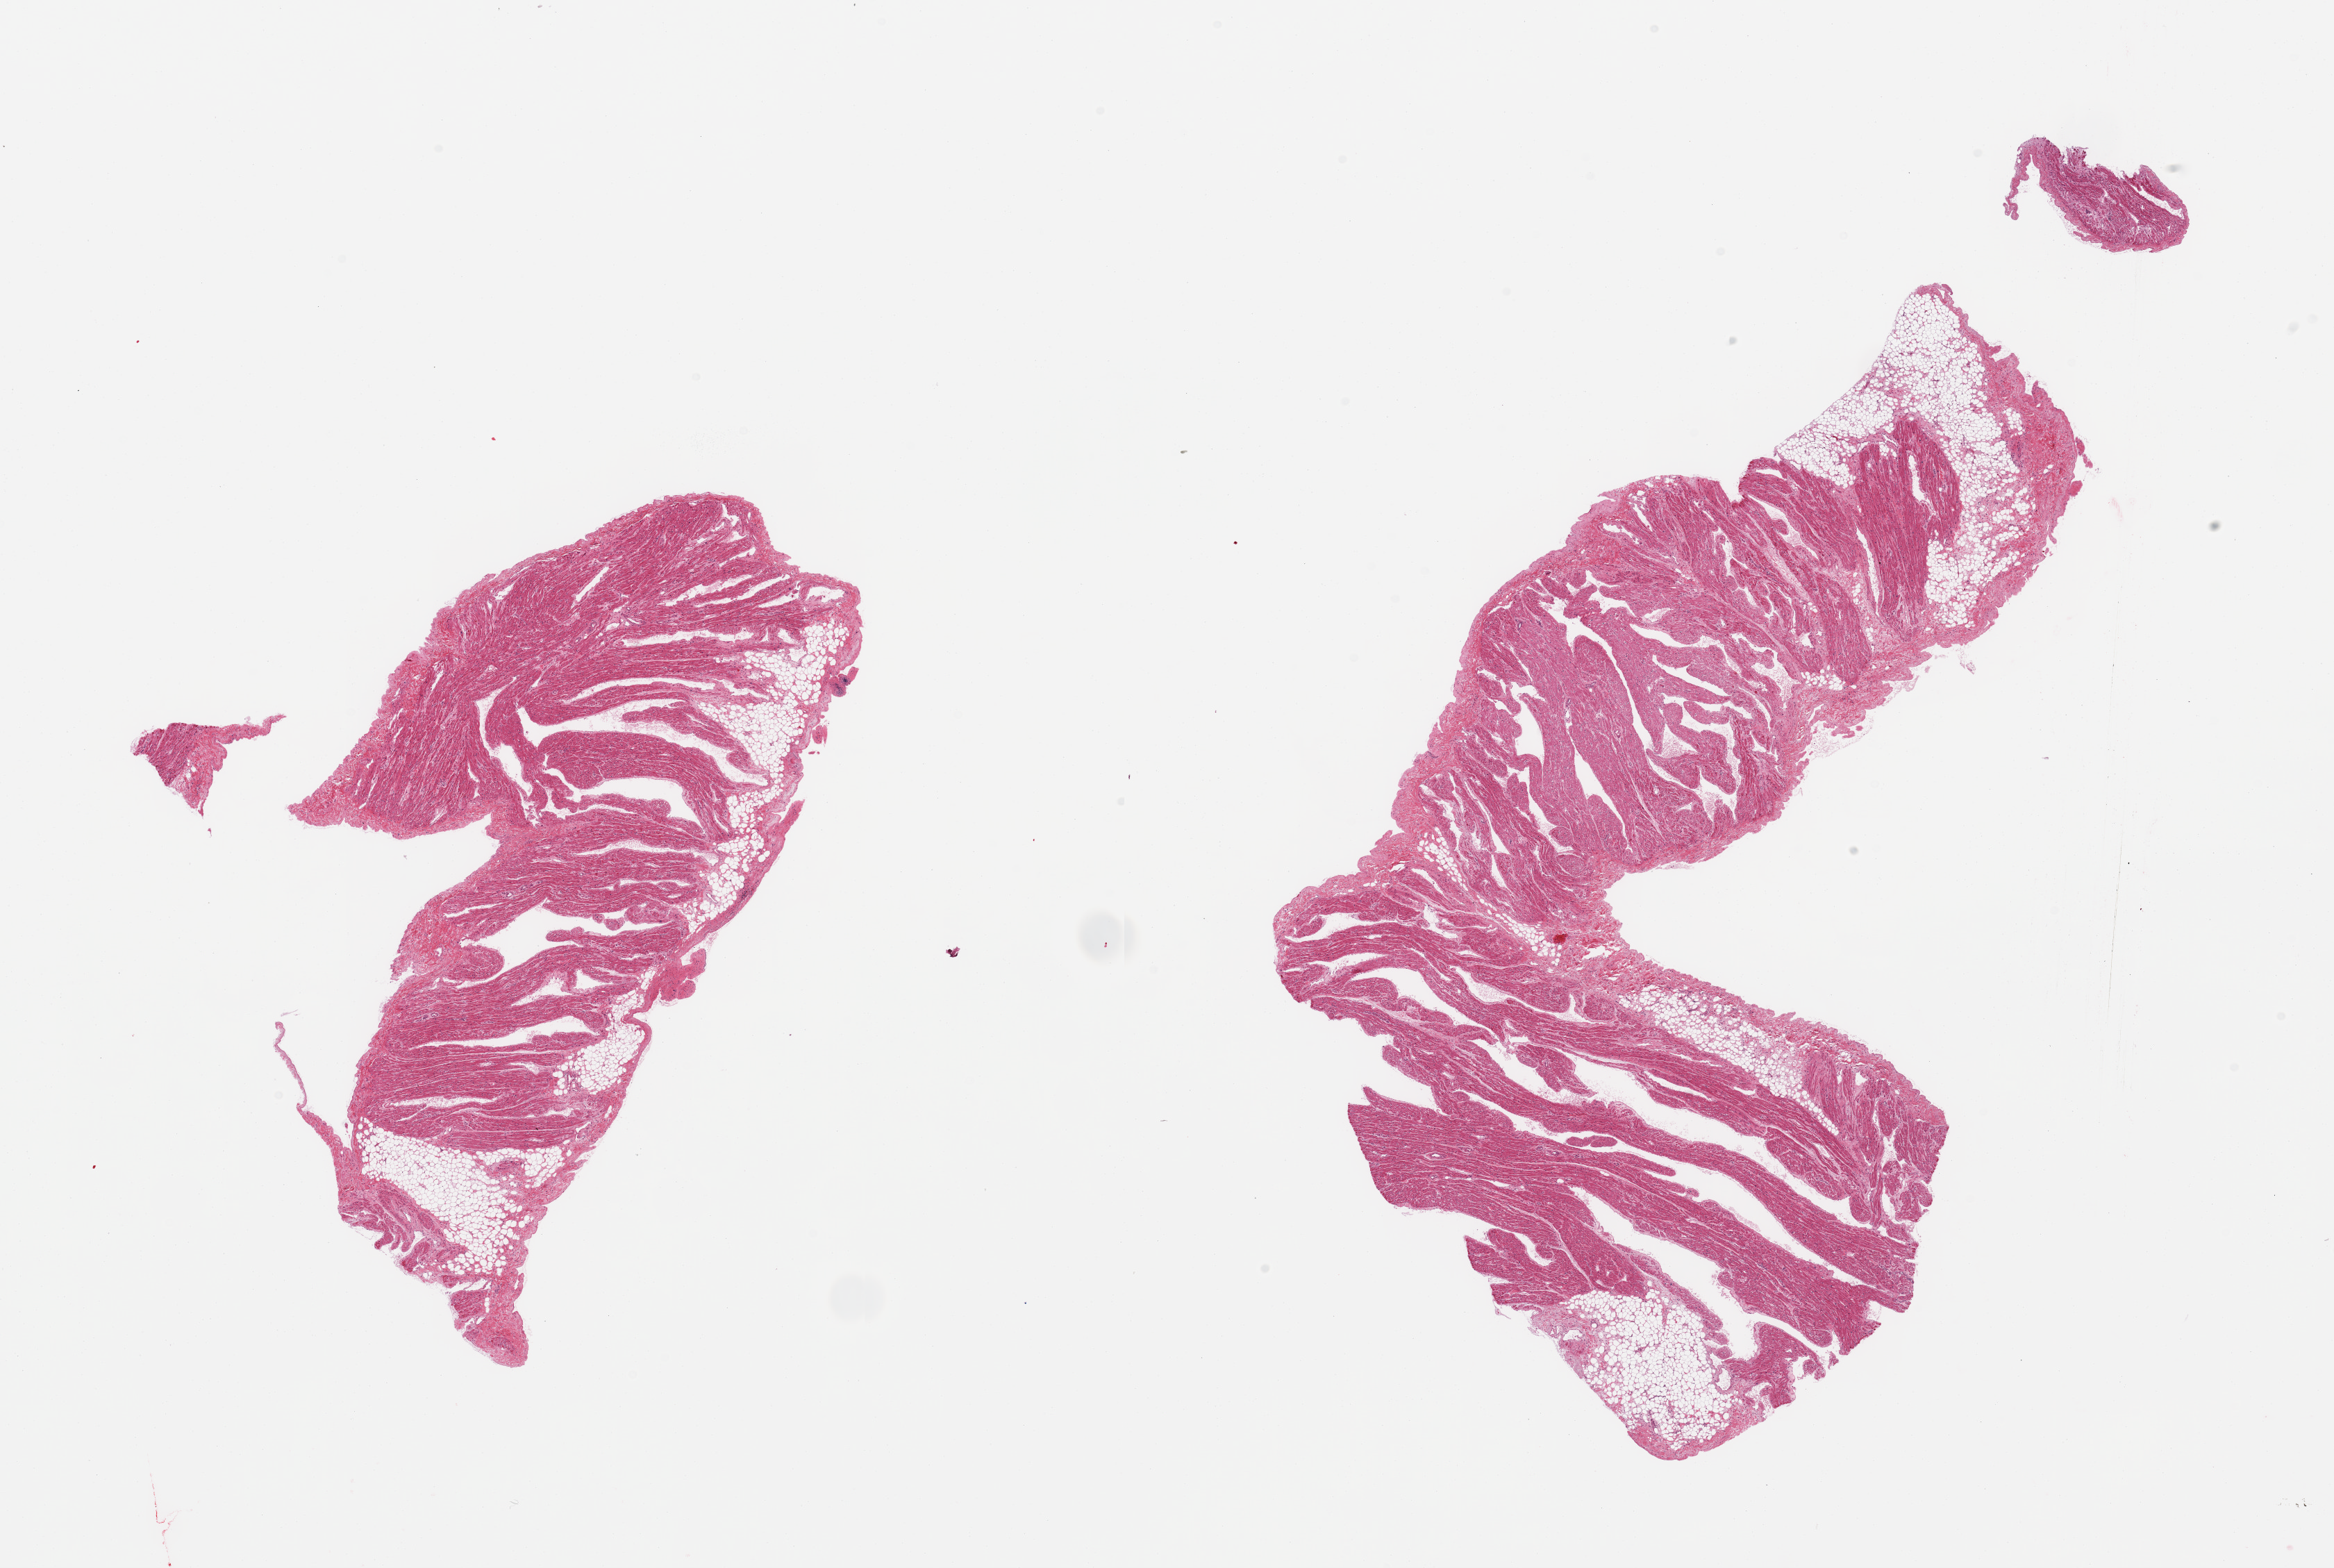
Digitized H&E-stained section — shown as a low-resolution overview of the whole scanned area (about 26.6 x 17.9 mm, from a 20x scan). PAXgene-fixed, paraffin-embedded tissue. Target tissue: auricular appendage. Tissue donor sample. Male donor.
Pathologist's review note for this sample: 2 pieces; includes 10-20% fat.